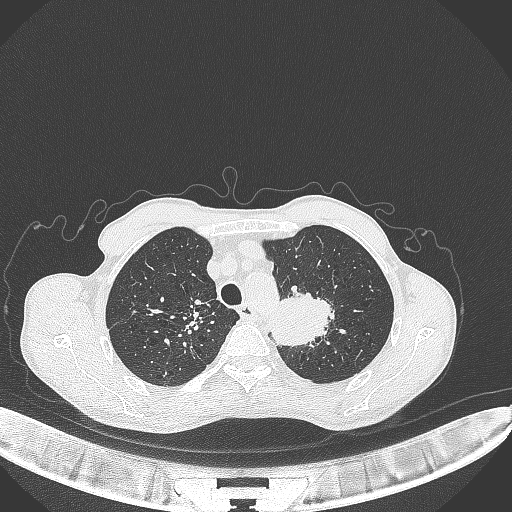
Chest CT, one axial slice. Slice 341 of 386 in the series (ordered by position). Reconstruction kernel B70f. Lung window (W 1500 / L -600 HU). 1 mm slice thickness. 512 × 512 image matrix. Male patient, age 65 years. From the clinical record (not read from this slice): clinical TNM (as recorded): T2b N0 M0; histopathological grade: G2.
Structures marked on this image (rectangle marked by the reading radiologist):
- lung tumour (recorded histology: adenocarcinoma): box from (x=269, y=292) to (x=337, y=348) px